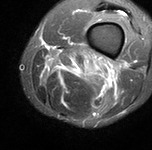
MRI of an extremity soft-tissue mass, one axial slice. Slice 21 of 90 in the series (ordered by position). STIR. MR volume resampled by the dataset authors to the PET/CT grid (not the native acquisition matrix). 3.27 mm slice thickness. 152 × 150 image matrix, field of view 148 × 146 mm. Male patient. From the clinical record (not read from this slice): histological type: undifferentiated pleomorphic liposarcoma; grade: high; site of the primary tumour: left thigh.
Outlined on this slice (expert contour drawn on MRI and transferred to this co-registered scan by the dataset authors):
- gross tumour volume including surrounding oedema: box from (x=41, y=51) to (x=119, y=88) px